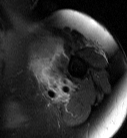
MRI of an extremity soft-tissue mass, one axial slice; T2-weighted fat-saturated; MR volume resampled by the dataset authors to the PET/CT grid (not the native acquisition matrix); 127 × 138 image matrix. Female patient. Case-level facts recorded for this patient, not image findings: histological type: pleiomorphic leiomyosarcoma; grade: high; site of the primary tumour: left biceps.
Outlined on this slice (expert contour drawn on MRI and transferred to this co-registered scan by the dataset authors):
- gross tumour volume including surrounding oedema: bounding box [x1, y1, x2, y2] px = [29, 36, 62, 88]
- gross tumour volume (mass): [29, 39, 60, 74]